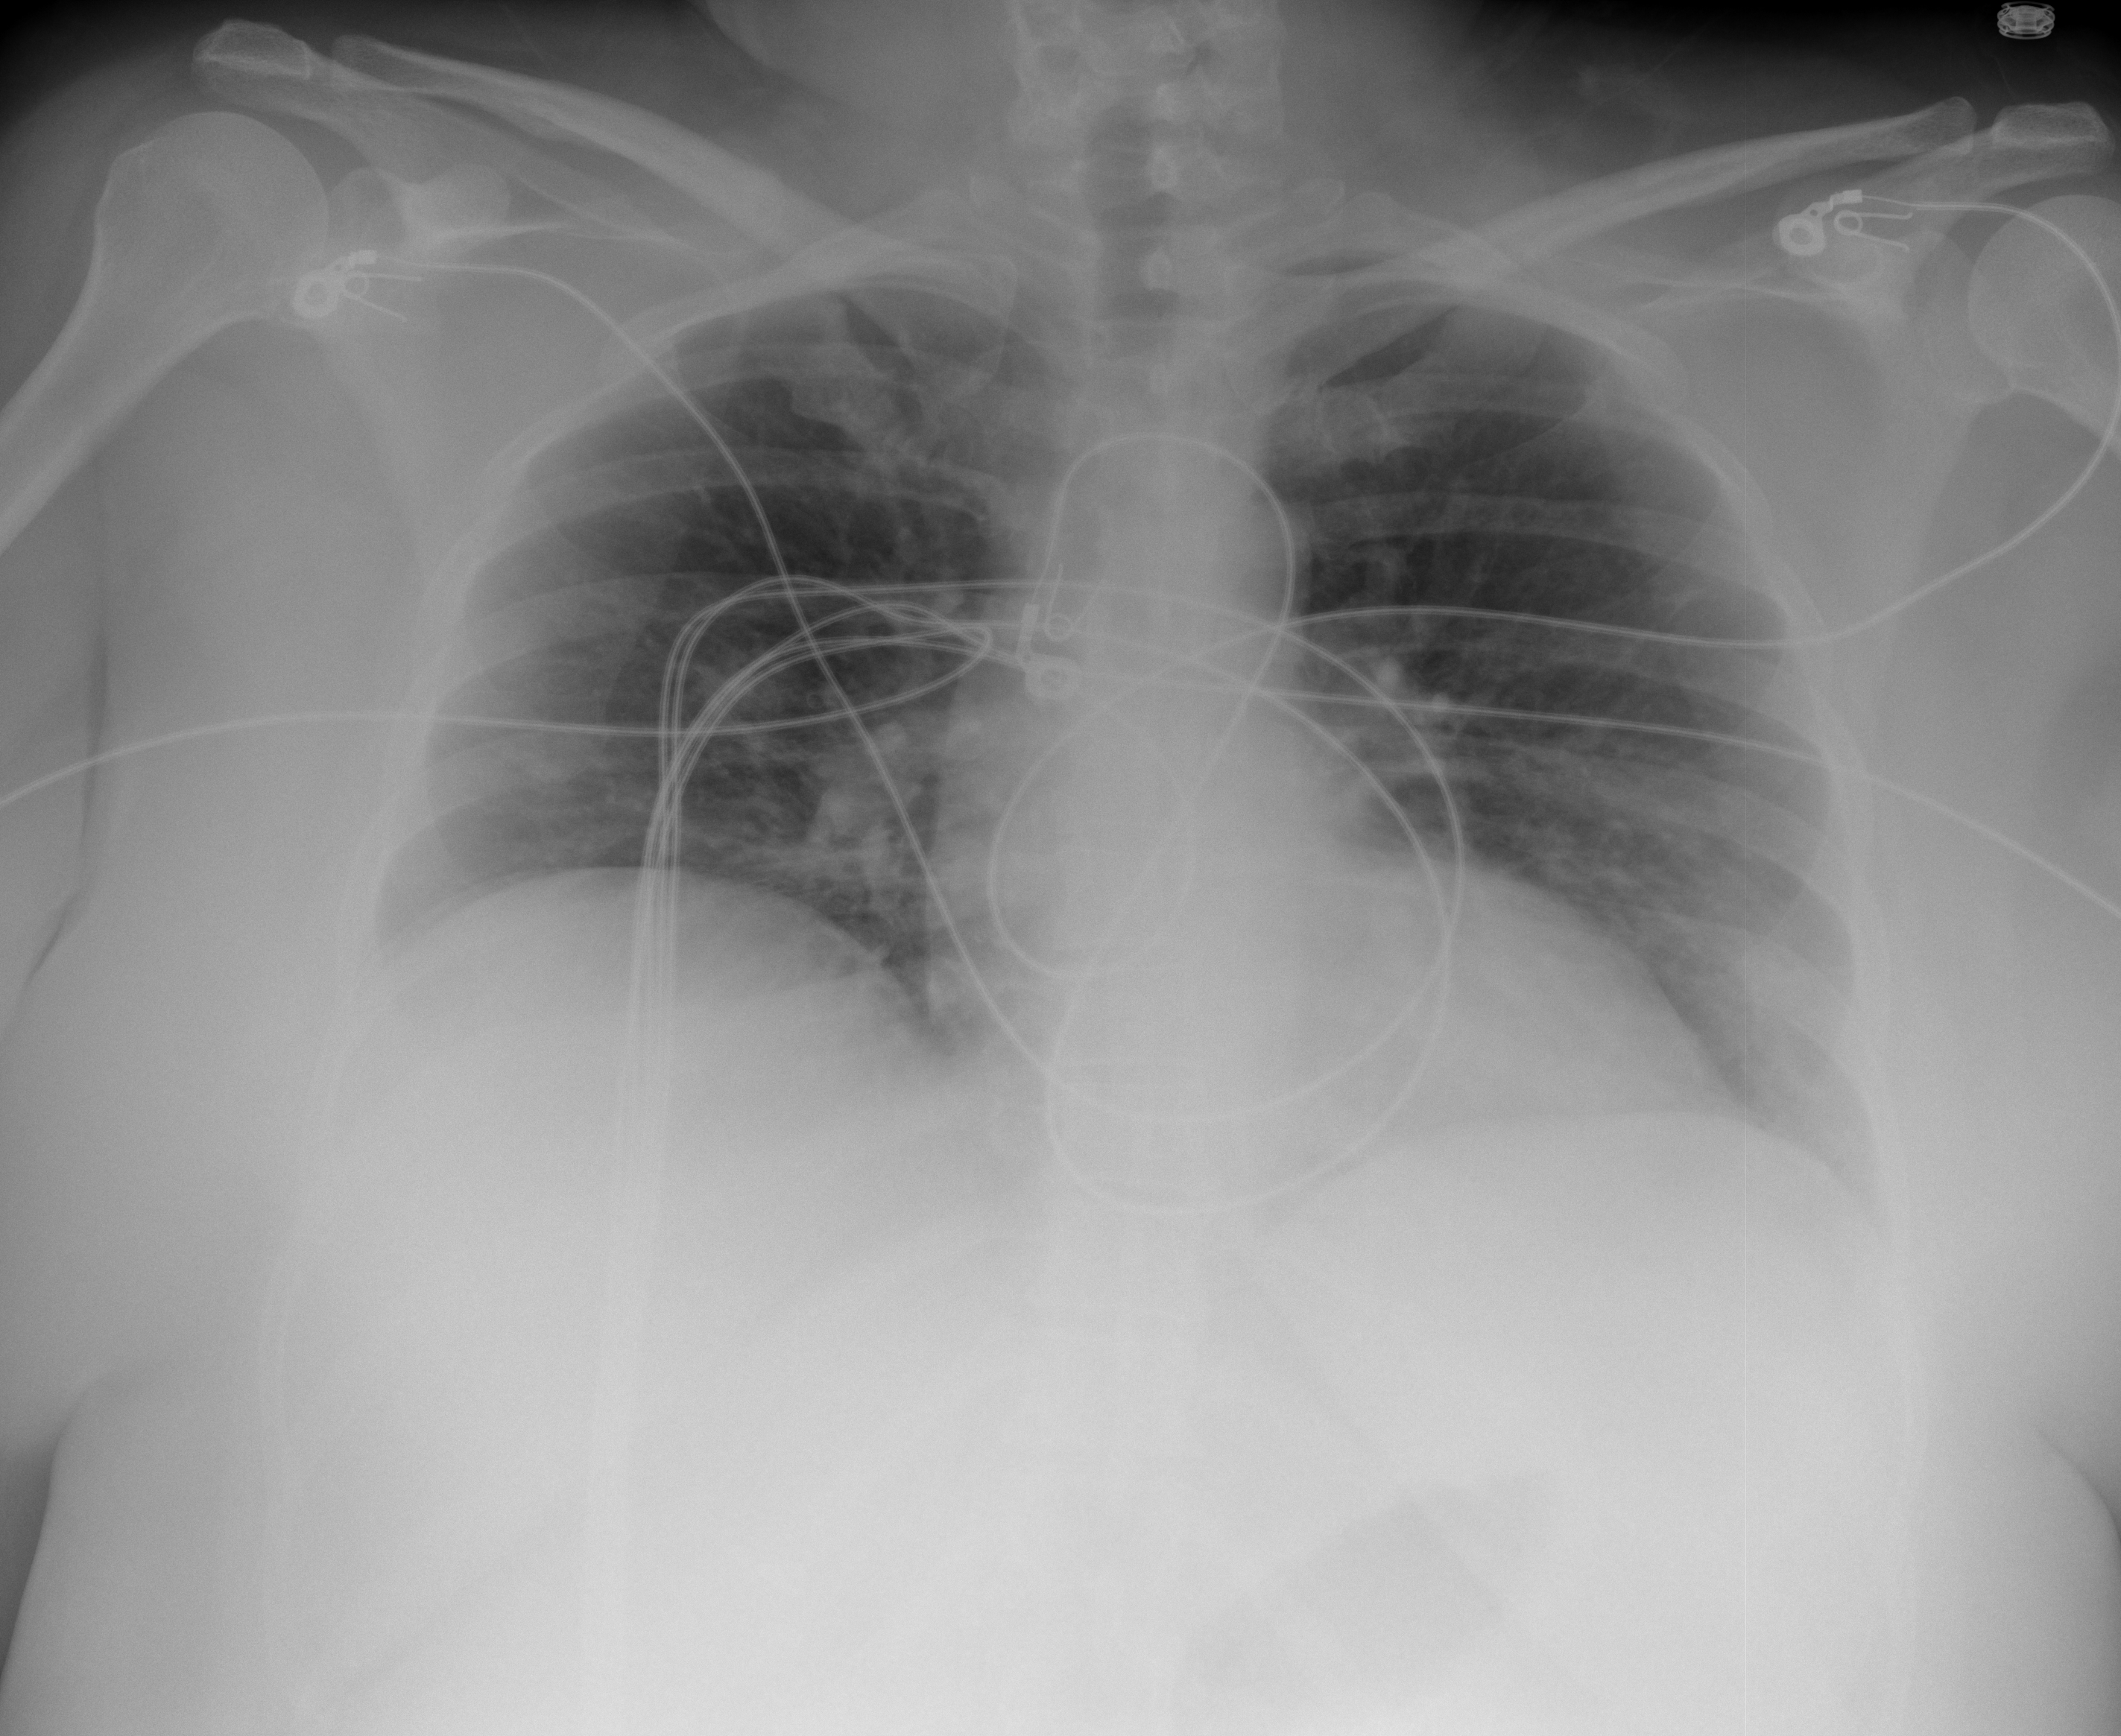
Portable chest radiograph, AP projection. Female patient, age 41 years; imaged 5 days after the COVID-19 diagnosis.
Radiologist key findings (as recorded): Hypoinflated lungs with minimal bibasilar opacities.